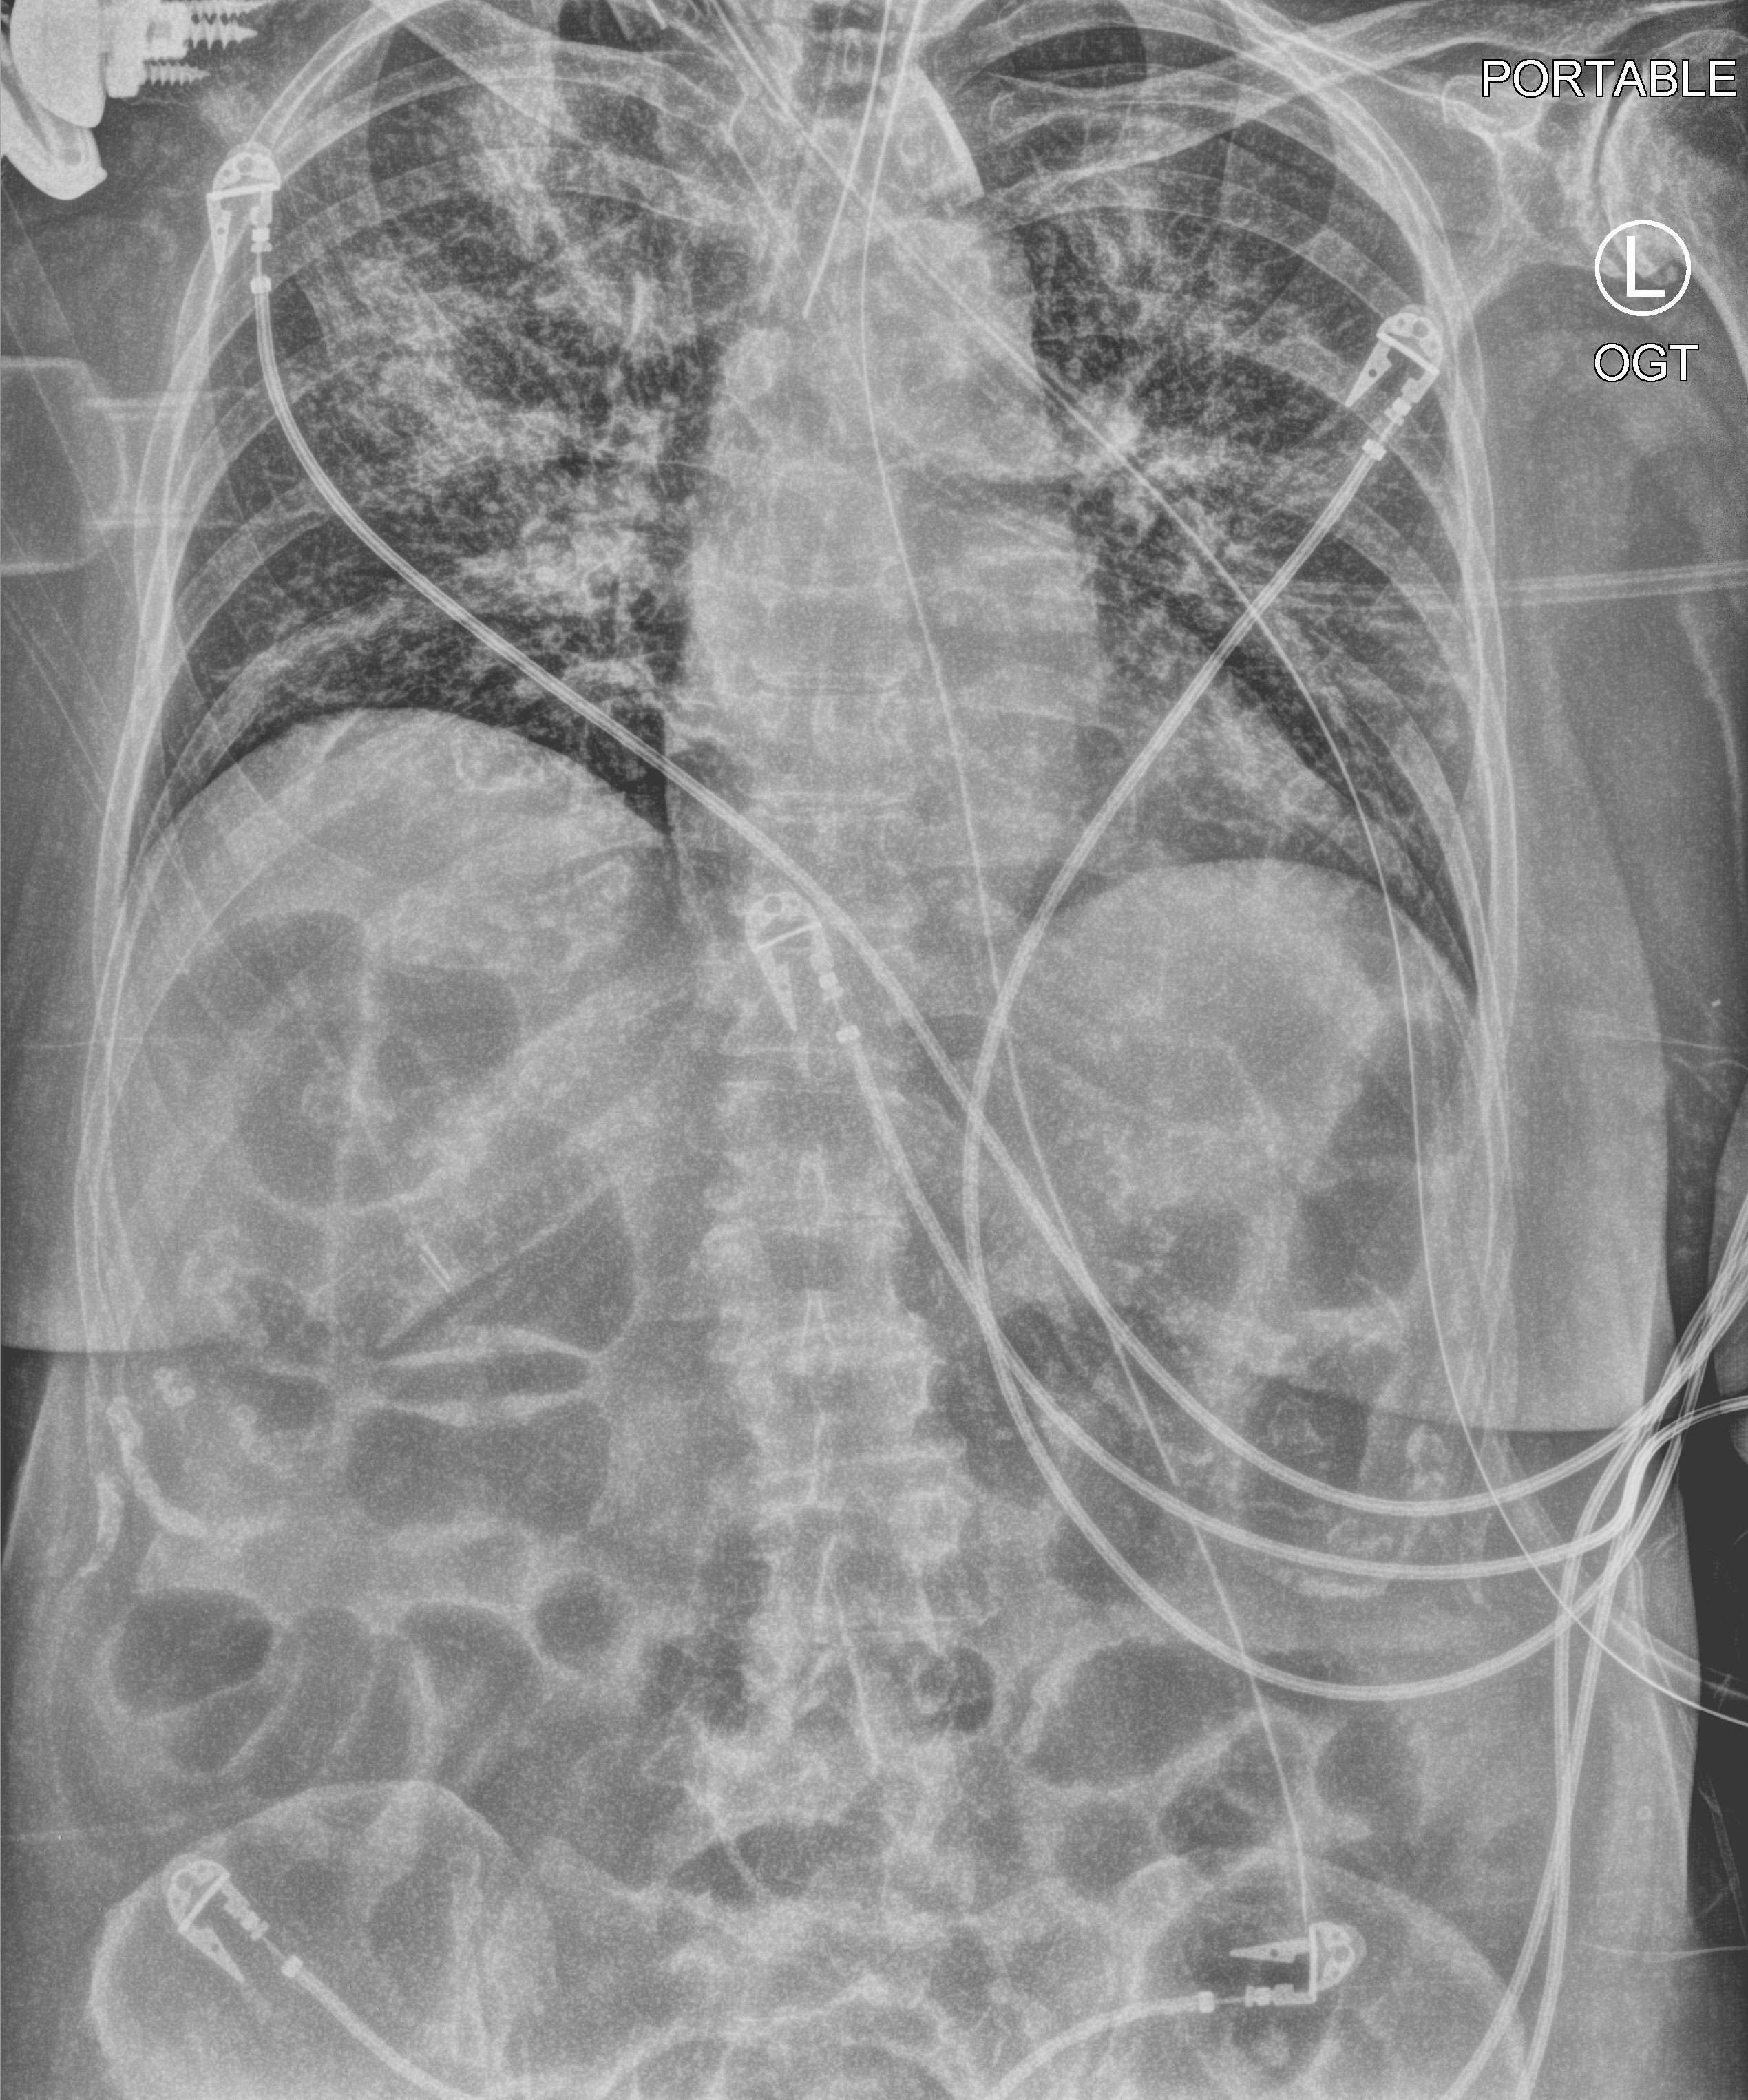
Portable chest radiograph. Female patient hospitalised with COVID-19, age 60–74 years.
Admission-level facts for this patient (not findings on this image; timing relative to this image not recorded): mechanically ventilated during this hospital stay: yes; length of hospital stay: 27 days.